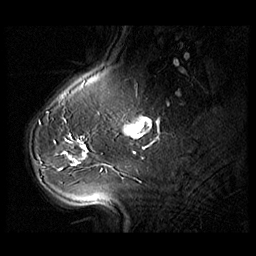
Breast MRI (dynamic contrast-enhanced), one sagittal slice. Slice 28 of 104 in the series (ordered by position). 3 images stored at this slice position (order not interpretable as contrast timing). 1.5 T. TE 1.3 ms, TR 5.5 ms. 256 × 256 image matrix, field of view 220 × 220 mm. Patient: female, 54 years. From the clinical record (not read from this slice): setting: breast cancer imaged before/during neoadjuvant chemotherapy; receptor status: HR-positive, HER2-negative.
Annotated regions visible in this slice (semi-automatically segmented with operator editing):
- analysis volume of interest (the breast-tissue region the enhancement analysis was run in; not a lesion): box from (x=28, y=127) to (x=104, y=182) px
- tumour enhancement mask (voxels above the 140 % enhancement threshold inside the analysis volume of interest): (x=61, y=140)–(x=88, y=155)